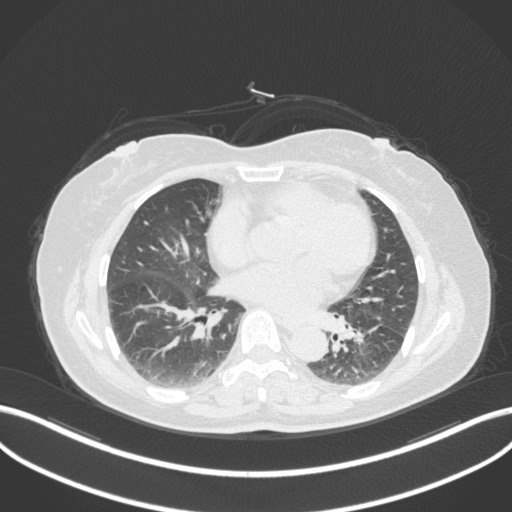
Chest CT, one axial slice; lung window (W 1500 / L -600 HU); 512 × 512 image matrix, field of view 400 × 400 mm. Patient: female, 59 years. From the clinical record (not read from this slice): clinical TNM (as recorded): T2a N0 M0; histopathological grade: G2-3.
Structures marked on this image (bounding box drawn by a radiologist):
- lung tumour (recorded histology: adenocarcinoma): bounding box (x1, y1, x2, y2) in pixels: (352, 321, 383, 351)